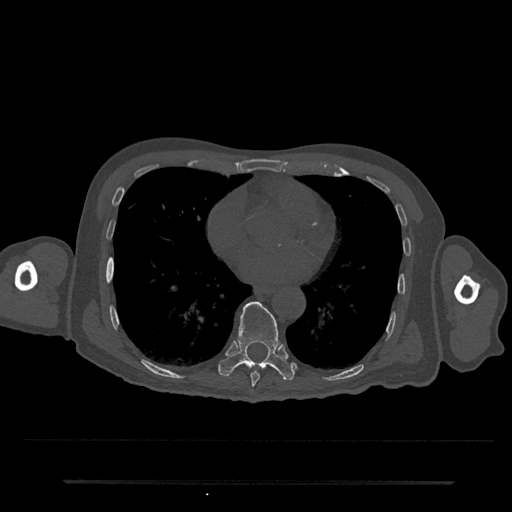
CT including the spine, one axial slice; position 383 of 797 along the scan axis; reconstruction kernel Br40s/3; 120 kVp; bone window (W 1800 / L 400 HU); 512 × 512 image matrix, field of view 427 × 427 mm. Patient: male, 74 years. From the clinical record (not read from this slice): primary cancer: prostate.
Outlined on this slice (semi-automatic segmentation, software-assisted and operator-edited):
- T8 vertebra: box from (x=250, y=371) to (x=260, y=392) px
- T9 vertebra: (x=218, y=301)–(x=295, y=380)